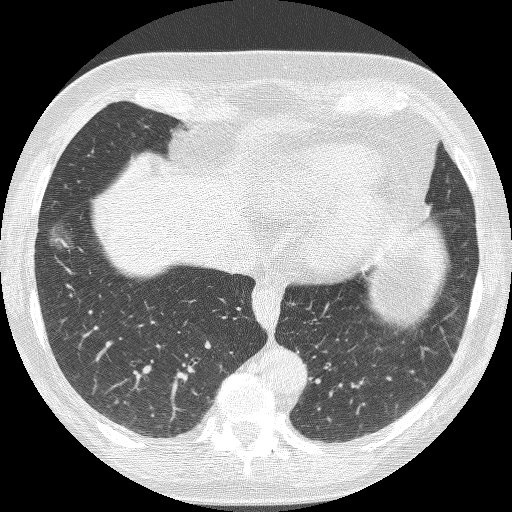
Chest CT (low-dose screening protocol), one axial image, baseline annual screen, lung window (W 1500 / L -600 HU), 120 kVp, 512 × 512 image matrix. Female, age 68 years at enrolment. Current smoker at enrolment.
• Expert reader's lesion annotation, bounding box (x1, y1, x2, y2) in pixels: (34, 220, 86, 270).
• Reader record for this screening exam (exam-level; its link to the box is not recorded): non-calcified nodule or mass ≥4 mm, right lower lobe, 16 × 12 mm, poorly defined margins, ground glass attenuation.
• Participant outcome: lung cancer diagnosed 406 days after this screen — bronchiolo-alveolar adenocarcinoma, NOS, right lower lobe, well differentiated (G1), stage IA (AJCC 6th edition), 13 mm at pathology.